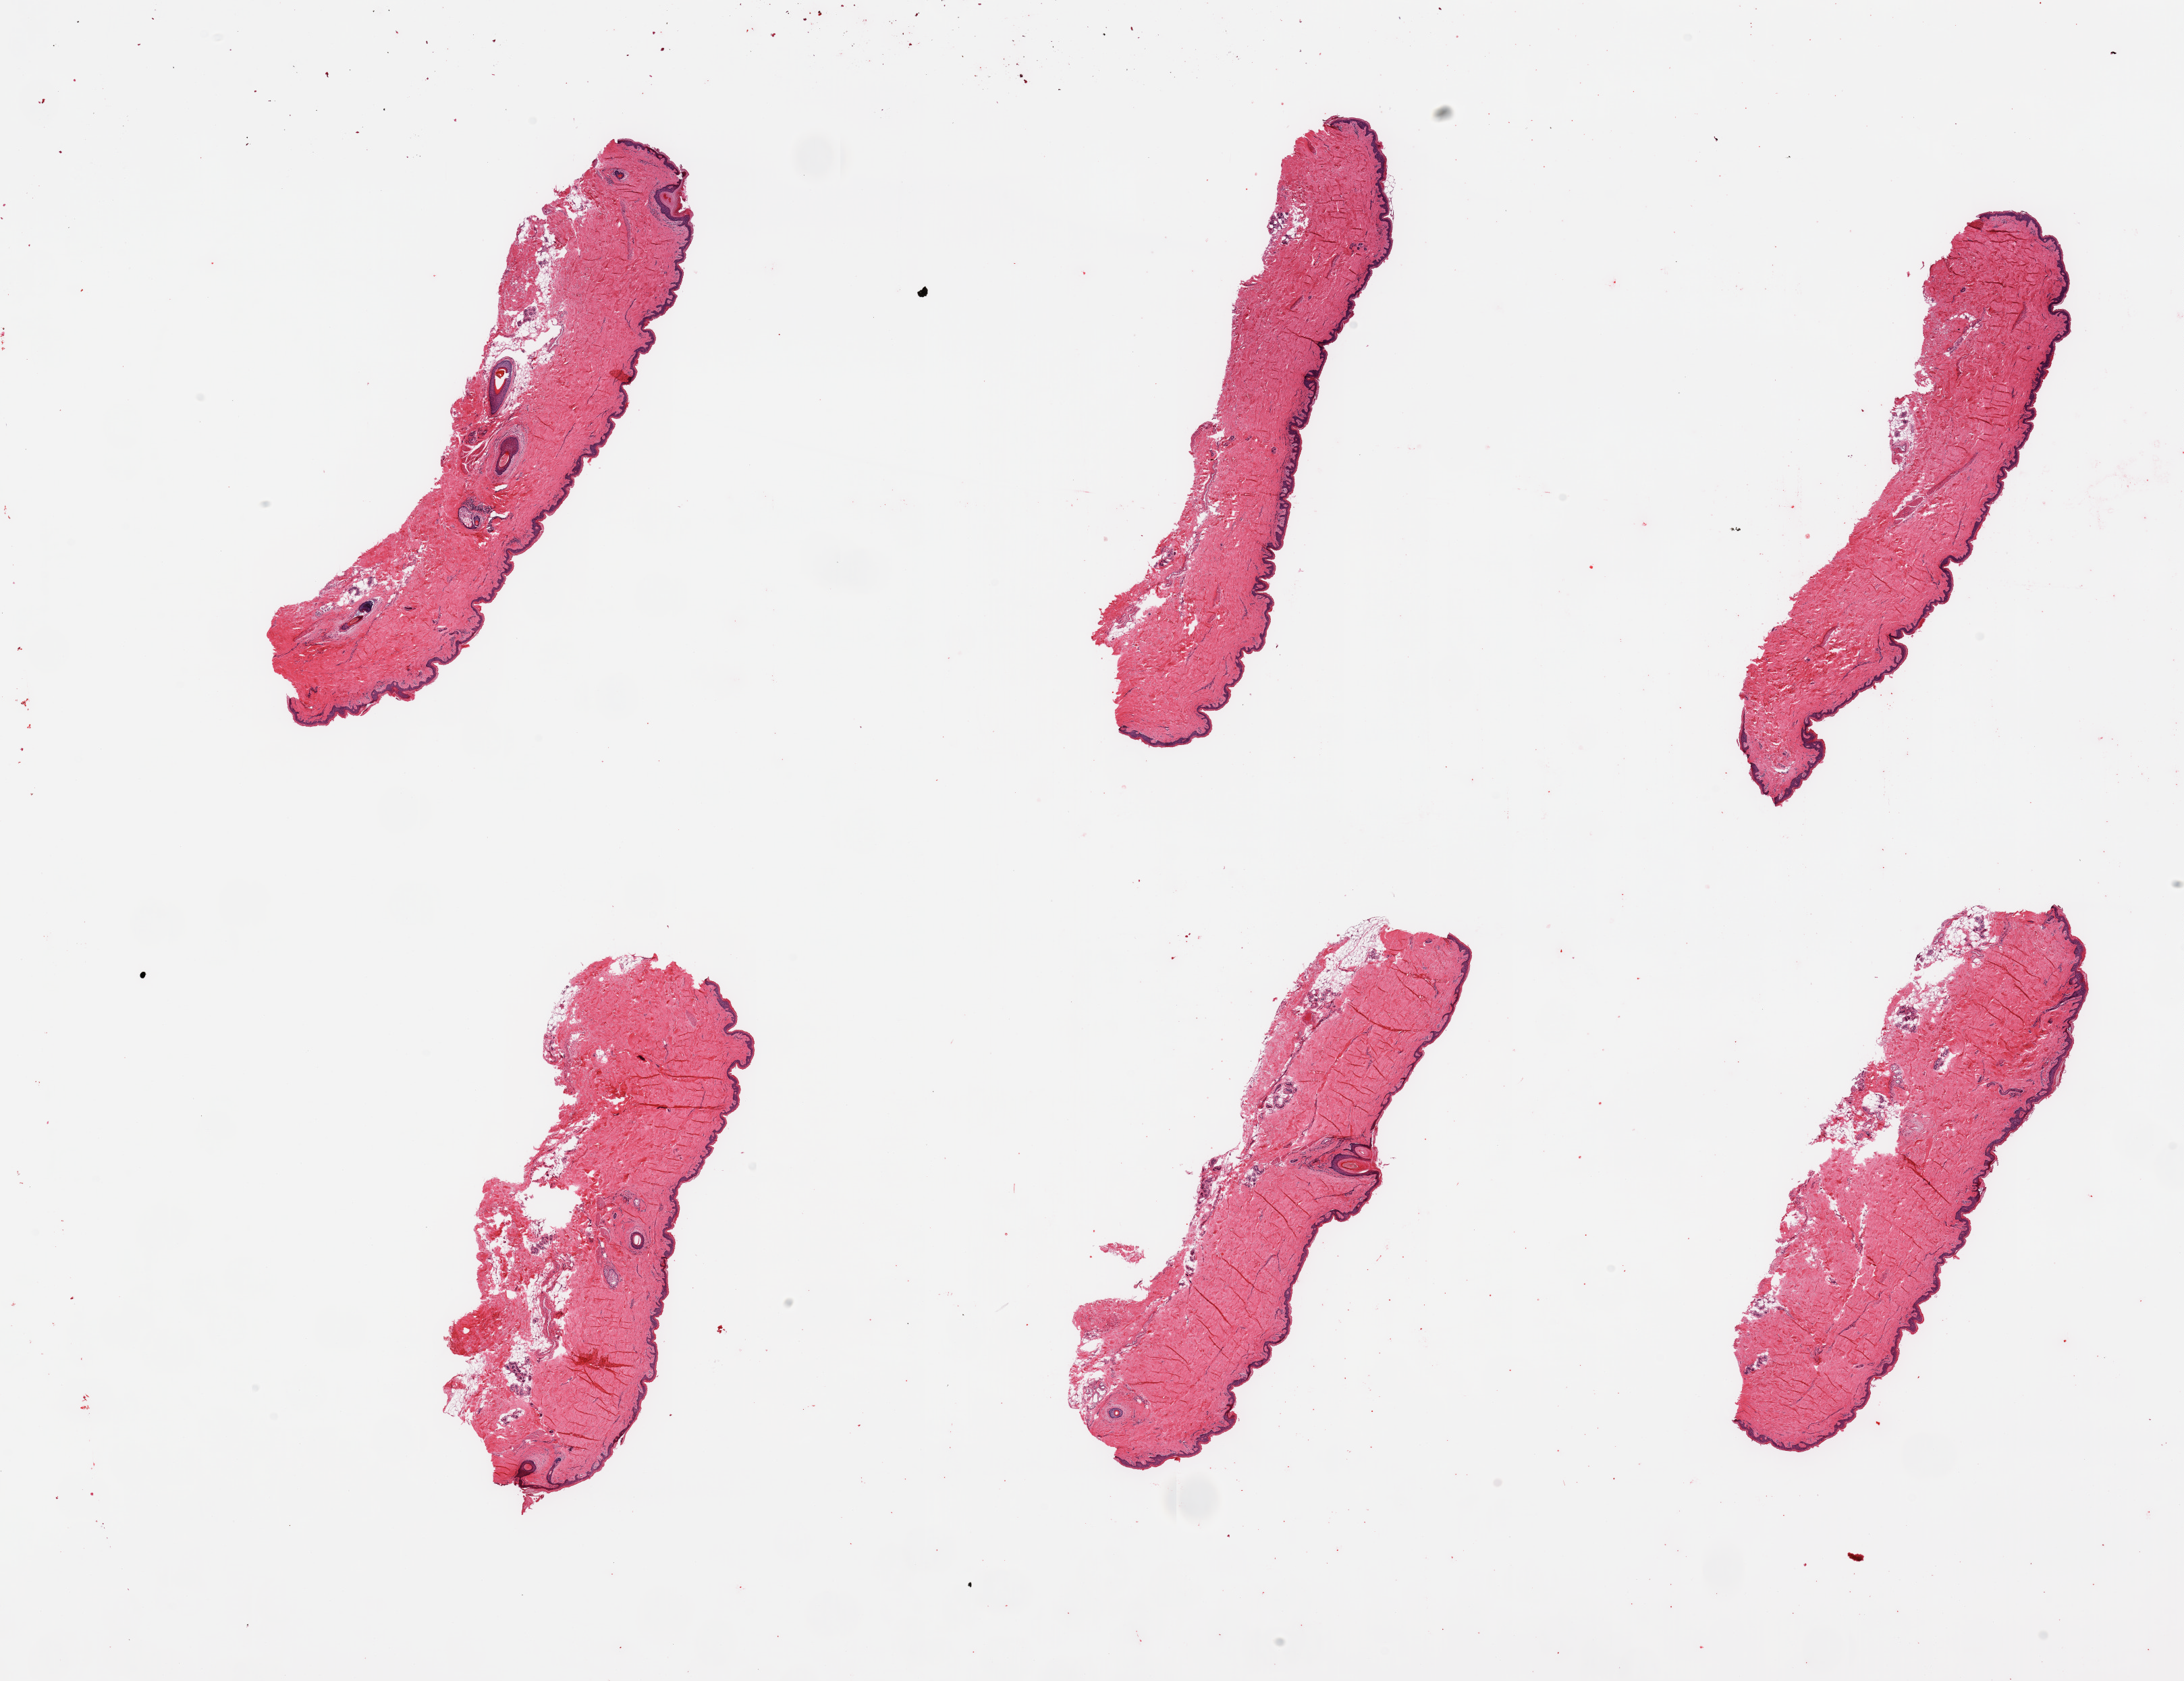
Digitized hematoxylin and eosin (H&E)-stained section, brightfield, whole scanned area (about 25.6 x 19.7 mm) shown as a low-resolution overview; PAXgene-fixed paraffin-embedded (PFPE) section; section of skin of suprapubic region (target tissue); tissue donor sample. Donor sex: female.
Review note (as recorded): 6 pieces; well trimmed; 5% dermal fat.